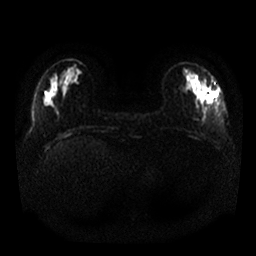
Breast MRI, one axial slice. Position 6 of 25 along the scan axis. Diffusion-weighted series; image 2 of 4 stored at this slice position (different b-values; order by instance number). 1.5 T. 256 × 256 image matrix, field of view 340 × 340 mm. Female patient.
Outlined on this slice (expert manual segmentation):
- tumour on diffusion-weighted imaging: bounding box (x1, y1, x2, y2) in pixels: (197, 75, 219, 105)